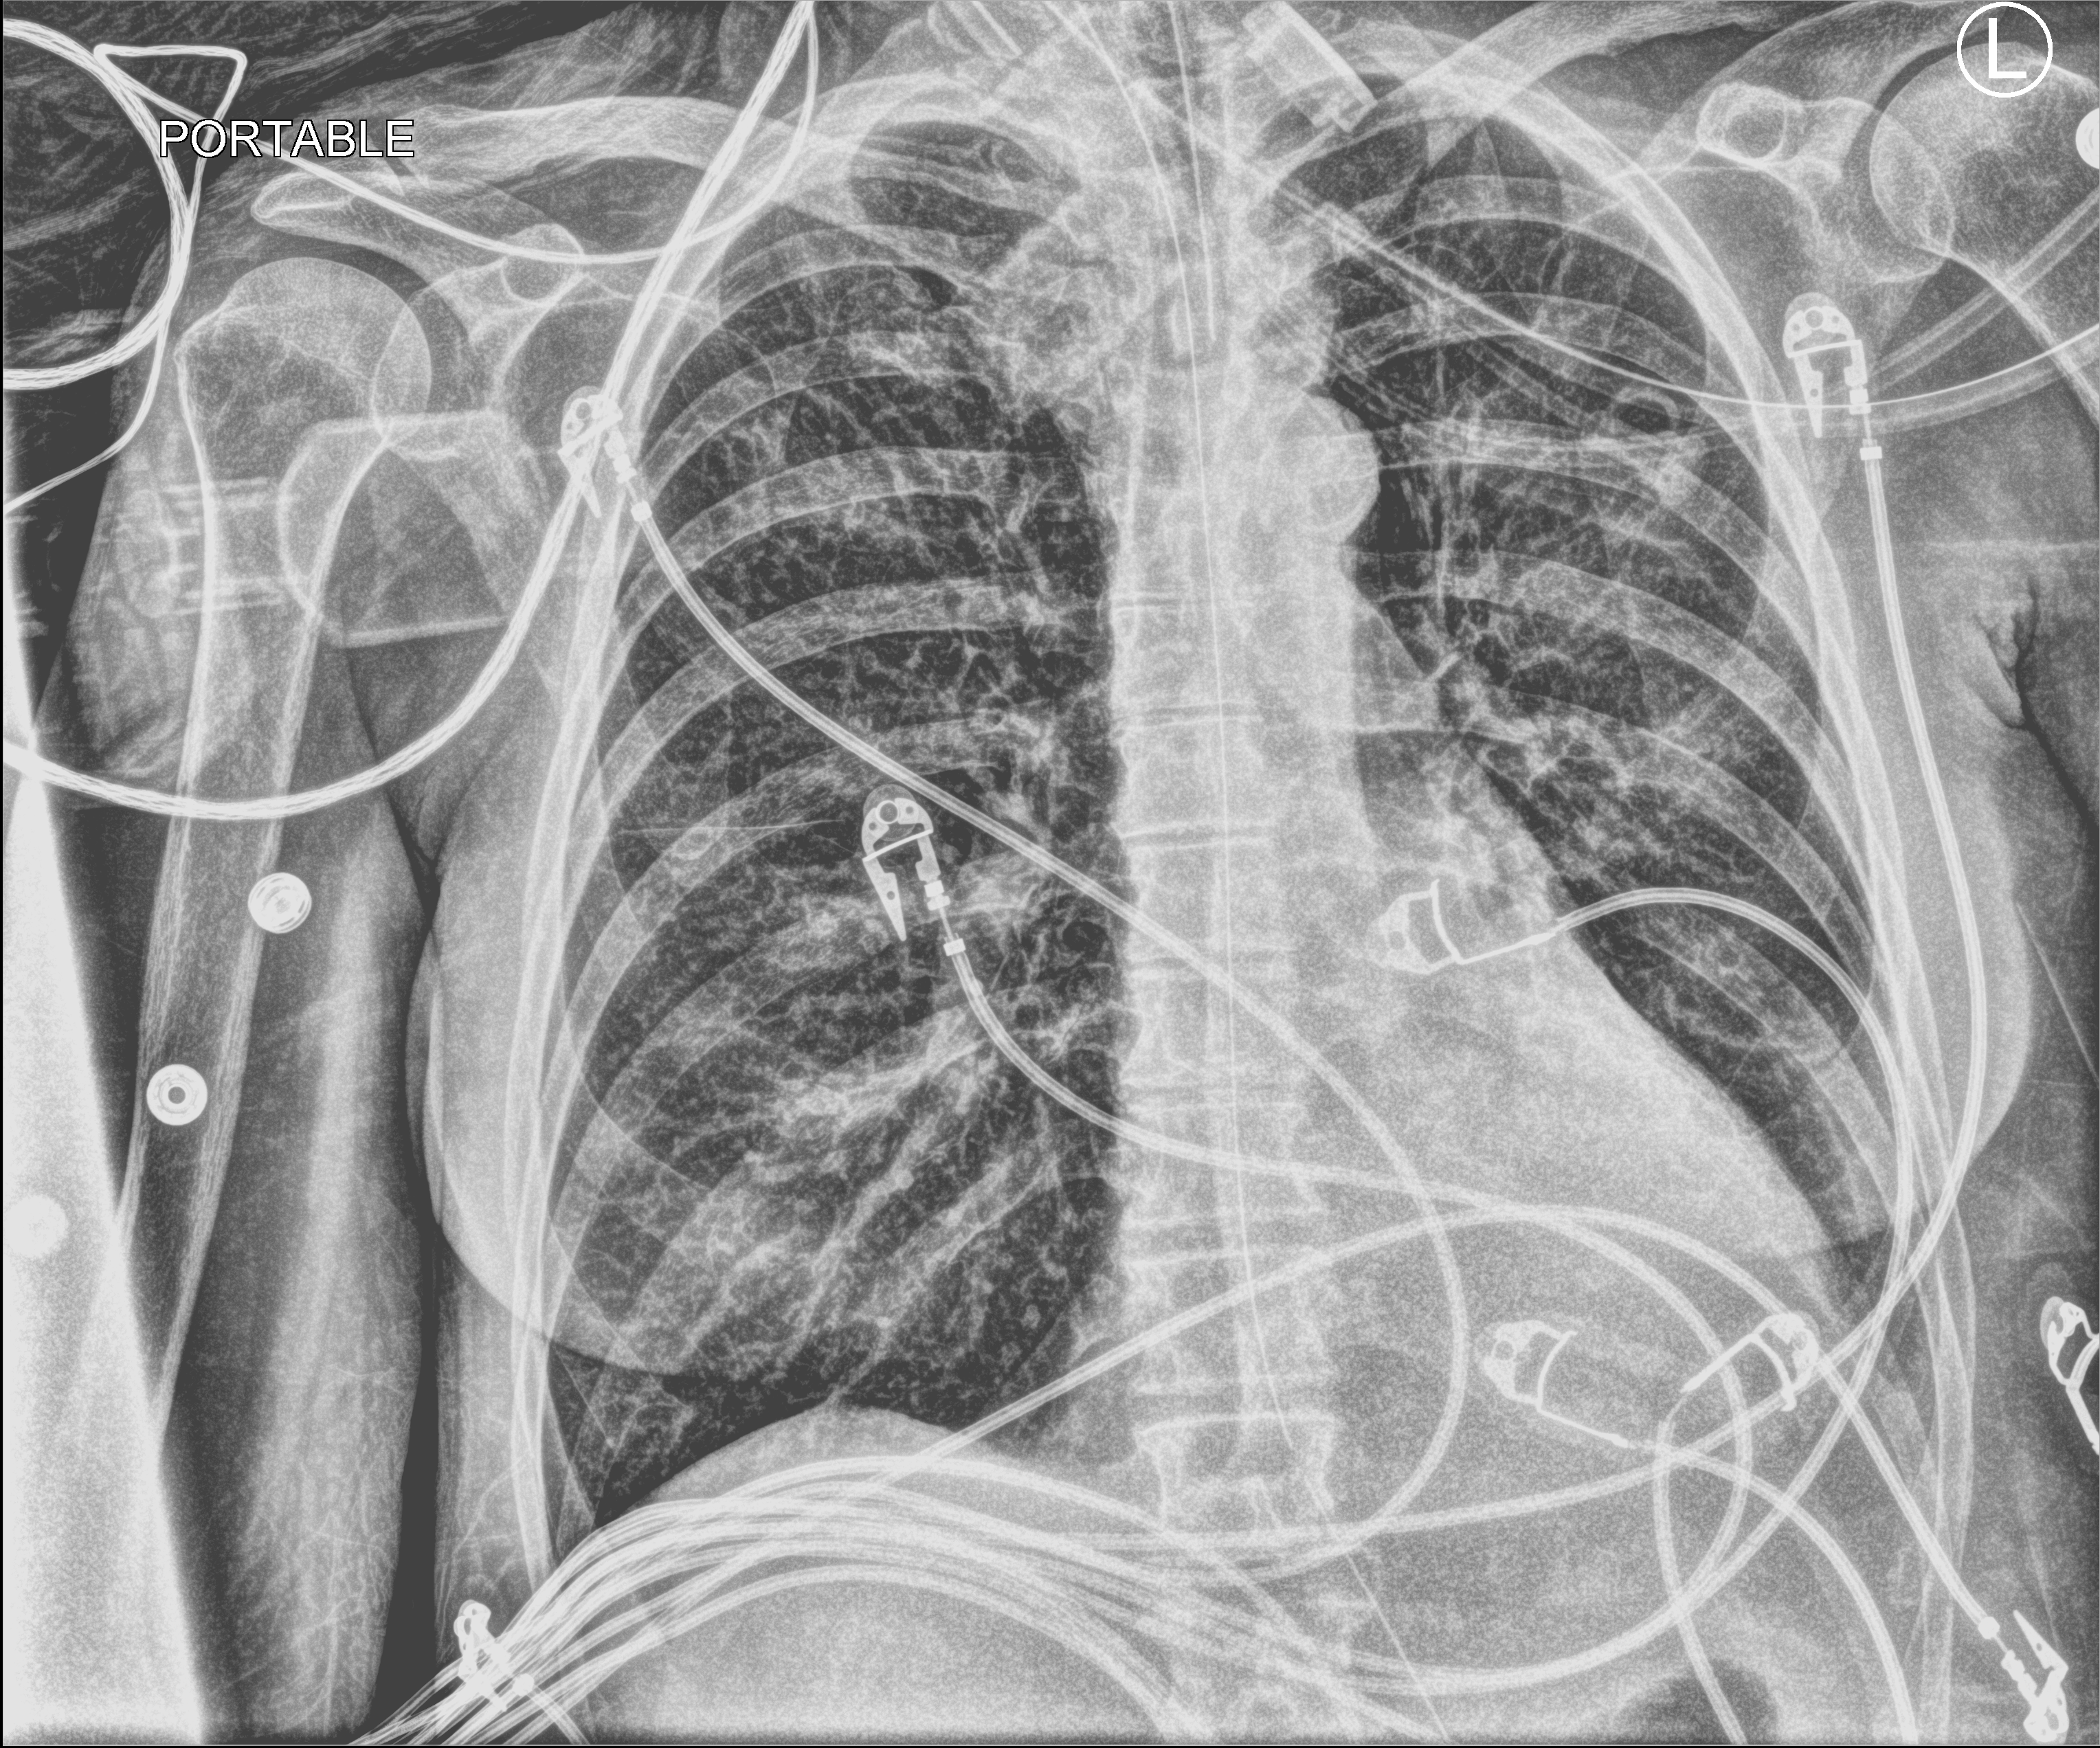
Bedside chest radiograph (computed radiography), anteroposterior (AP) projection. Female patient hospitalised with COVID-19, age 60–74 years.
From the hospital-stay record, not from the radiograph (when in the stay this image was taken is not recorded):
- admitted to intensive care during this hospital stay: yes